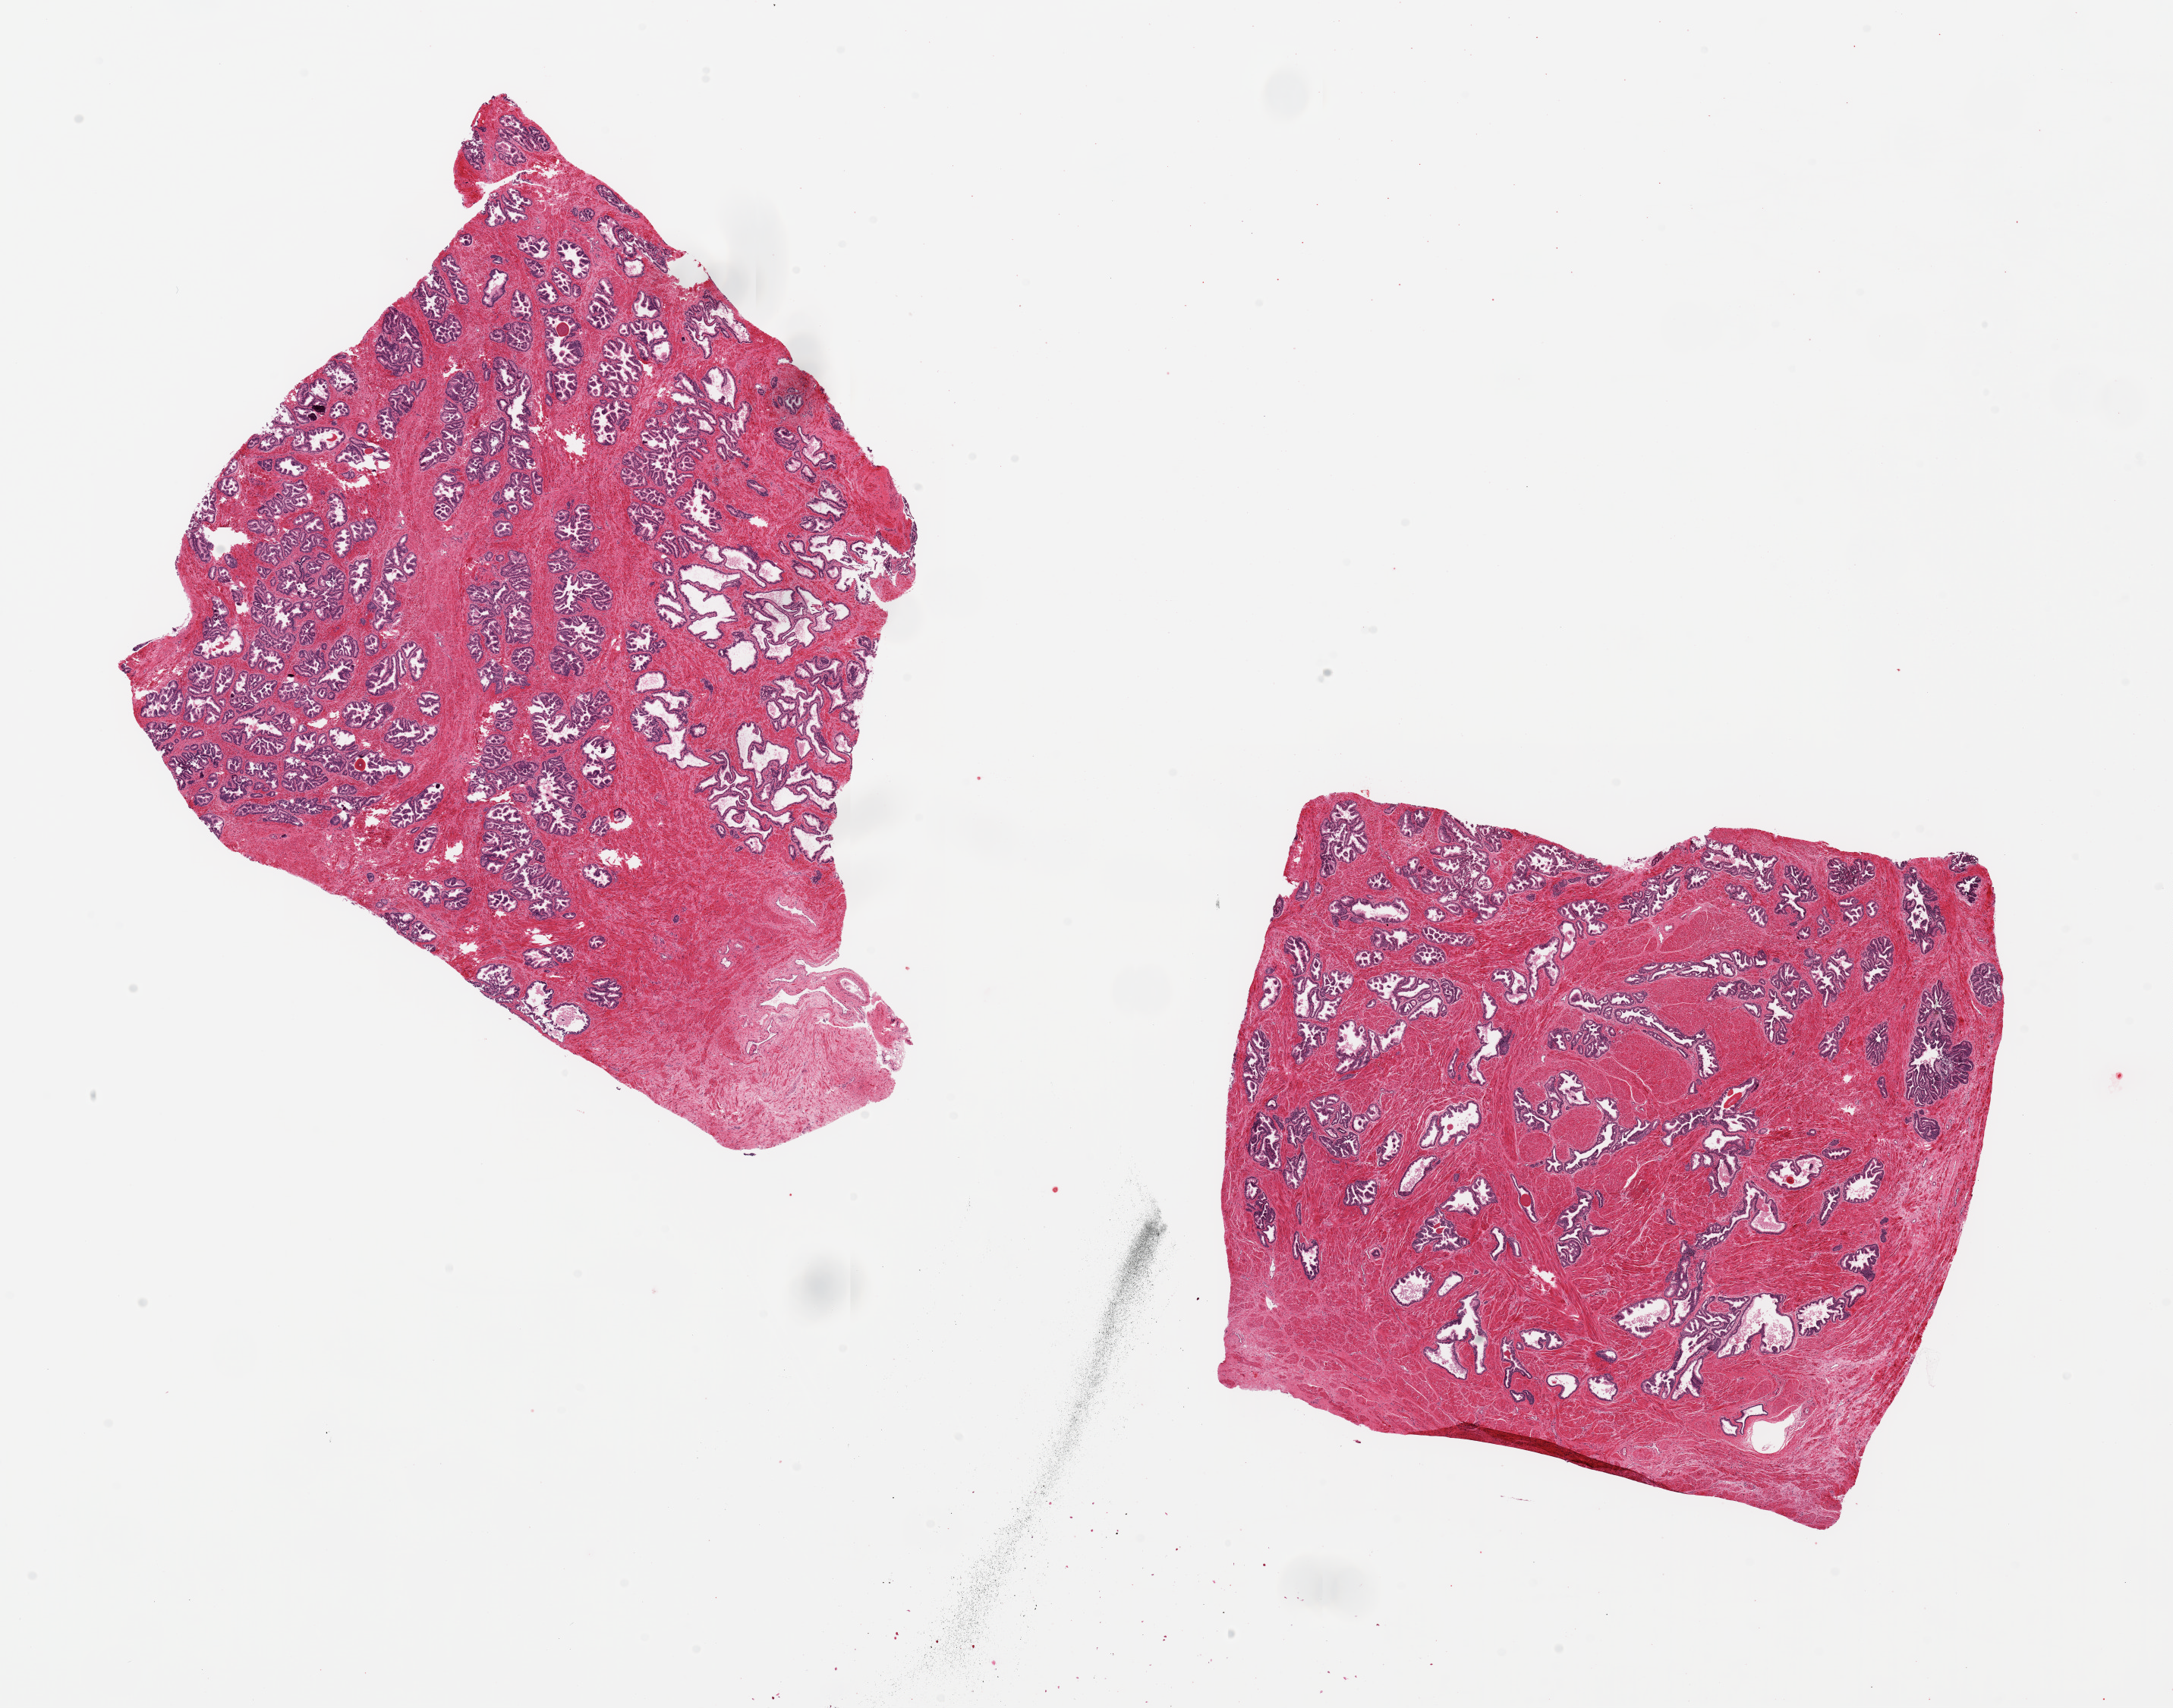
Digitized hematoxylin and eosin (H&E)-stained section, whole scanned area (about 22.6 x 17.8 mm) shown as a low-resolution overview, PAXgene-fixed paraffin-embedded (PFPE) section, sampled site (target tissue): prostate, donor tissue sample. Donor sex: male.
• reviewer comment on this tissue sample: 2 pieces ~8x7mm. Glandular mucosa extremely well preserved